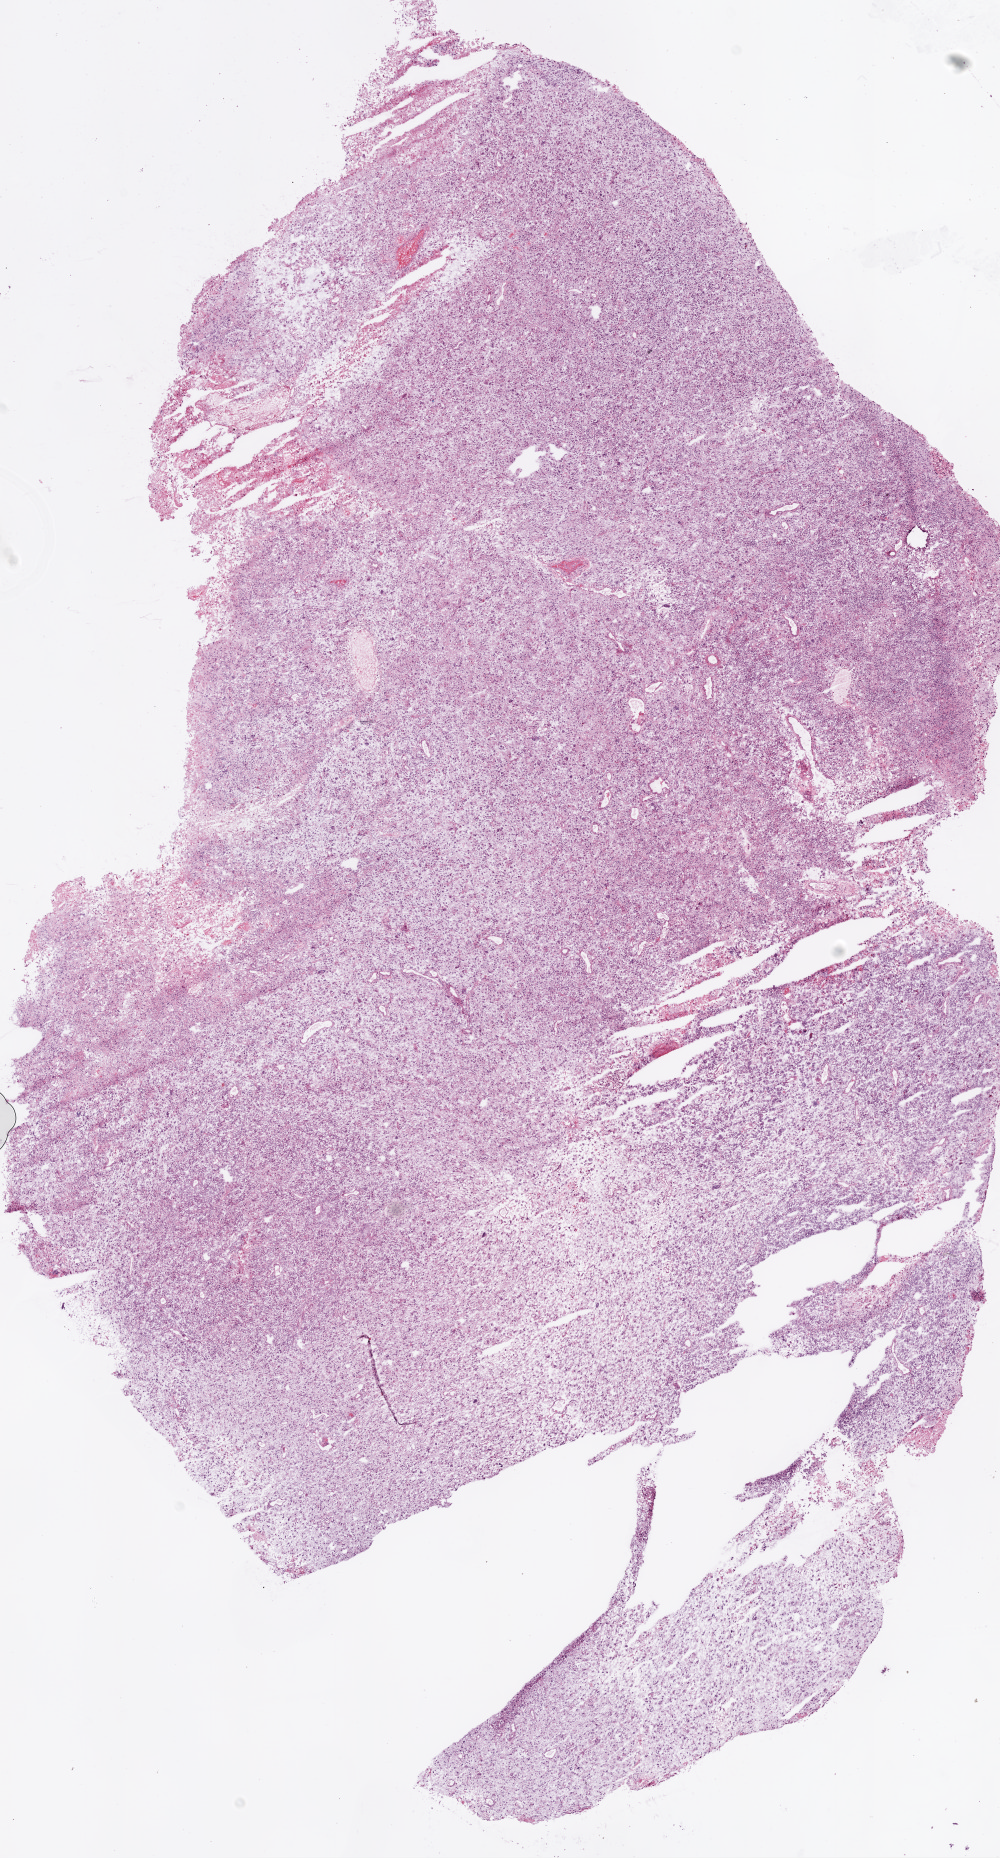
Whole-slide histology image, H&E-stained, shown as a low-resolution overview of the whole scanned area (about 8.0 x 14.9 mm), frozen section, sample: primary tumour, brain. Patient: female, age at initial diagnosis 75 years. Slide review estimates, as recorded: tumour cells 85%, tumour nuclei 95%, normal cells 0%, stromal cells 5%, necrosis 10%.
- diagnosis: Glioblastoma